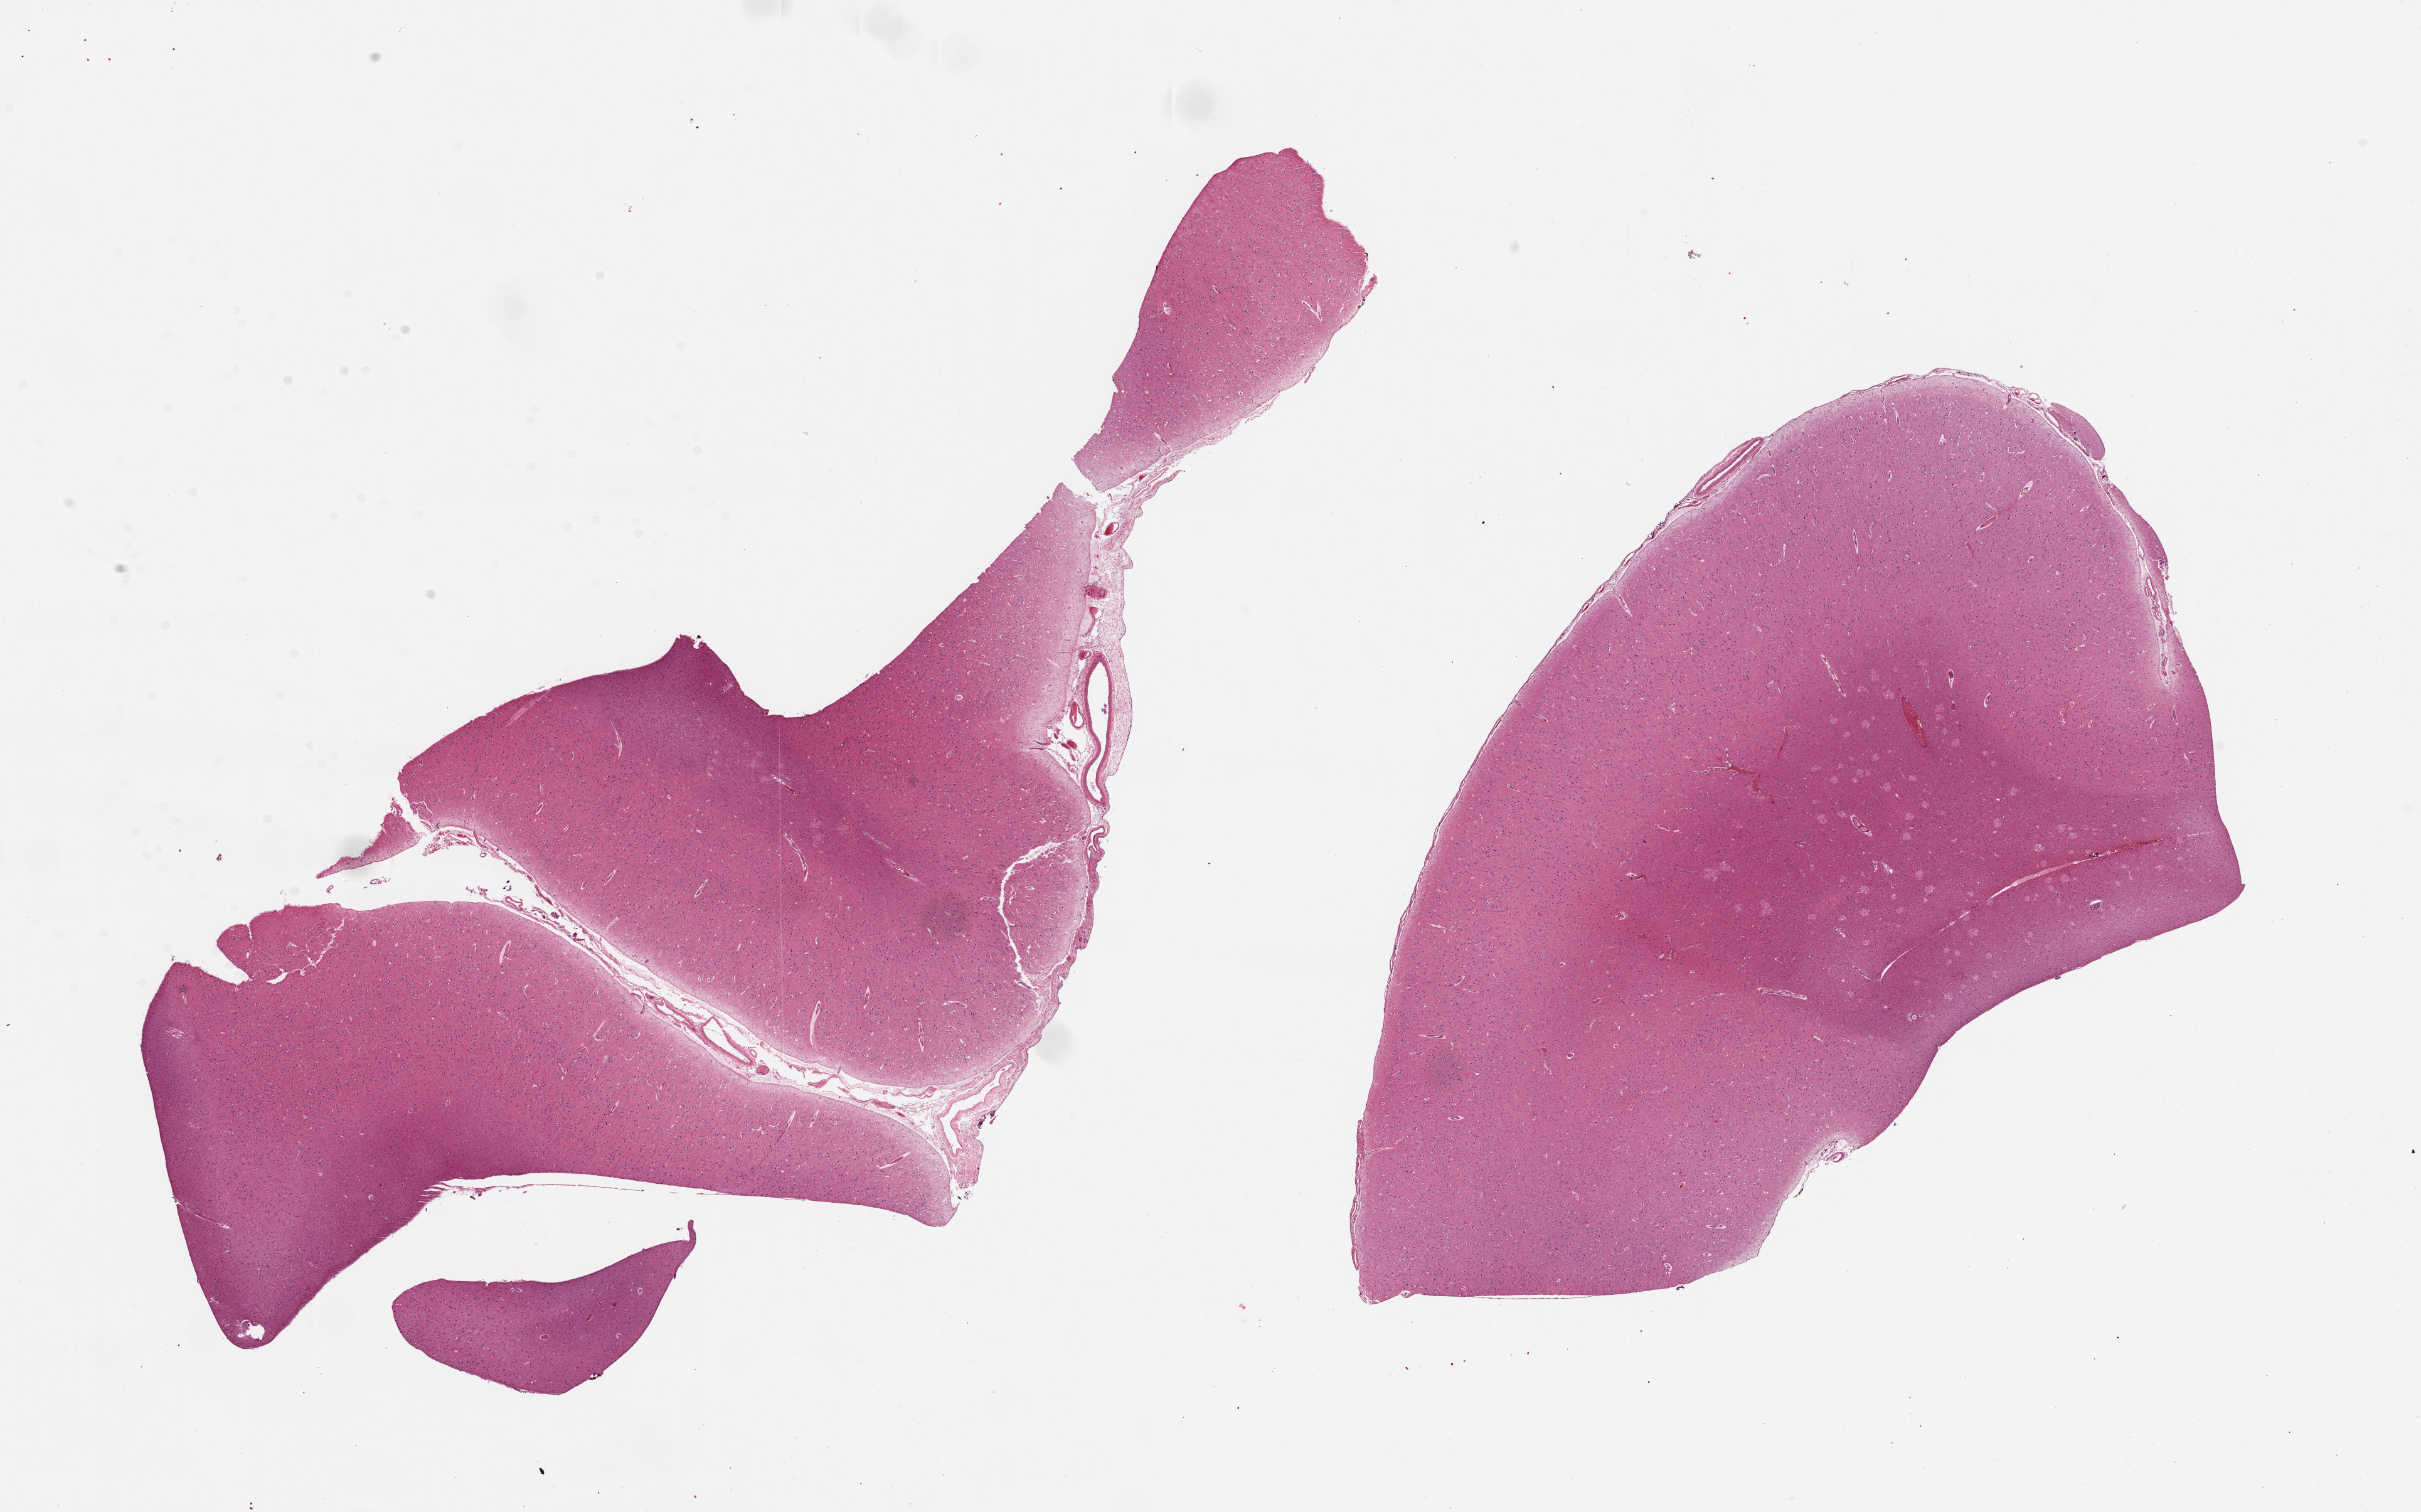
Digitized H&E-stained section — a low-resolution overview of the entire scanned area, about 30.5 x 19.1 mm, PAXgene-fixed, paraffin-embedded tissue, target tissue: cerebral cortex, donor tissue sample. Male donor.
Review note (as recorded): 2 piece, no abnormalities.